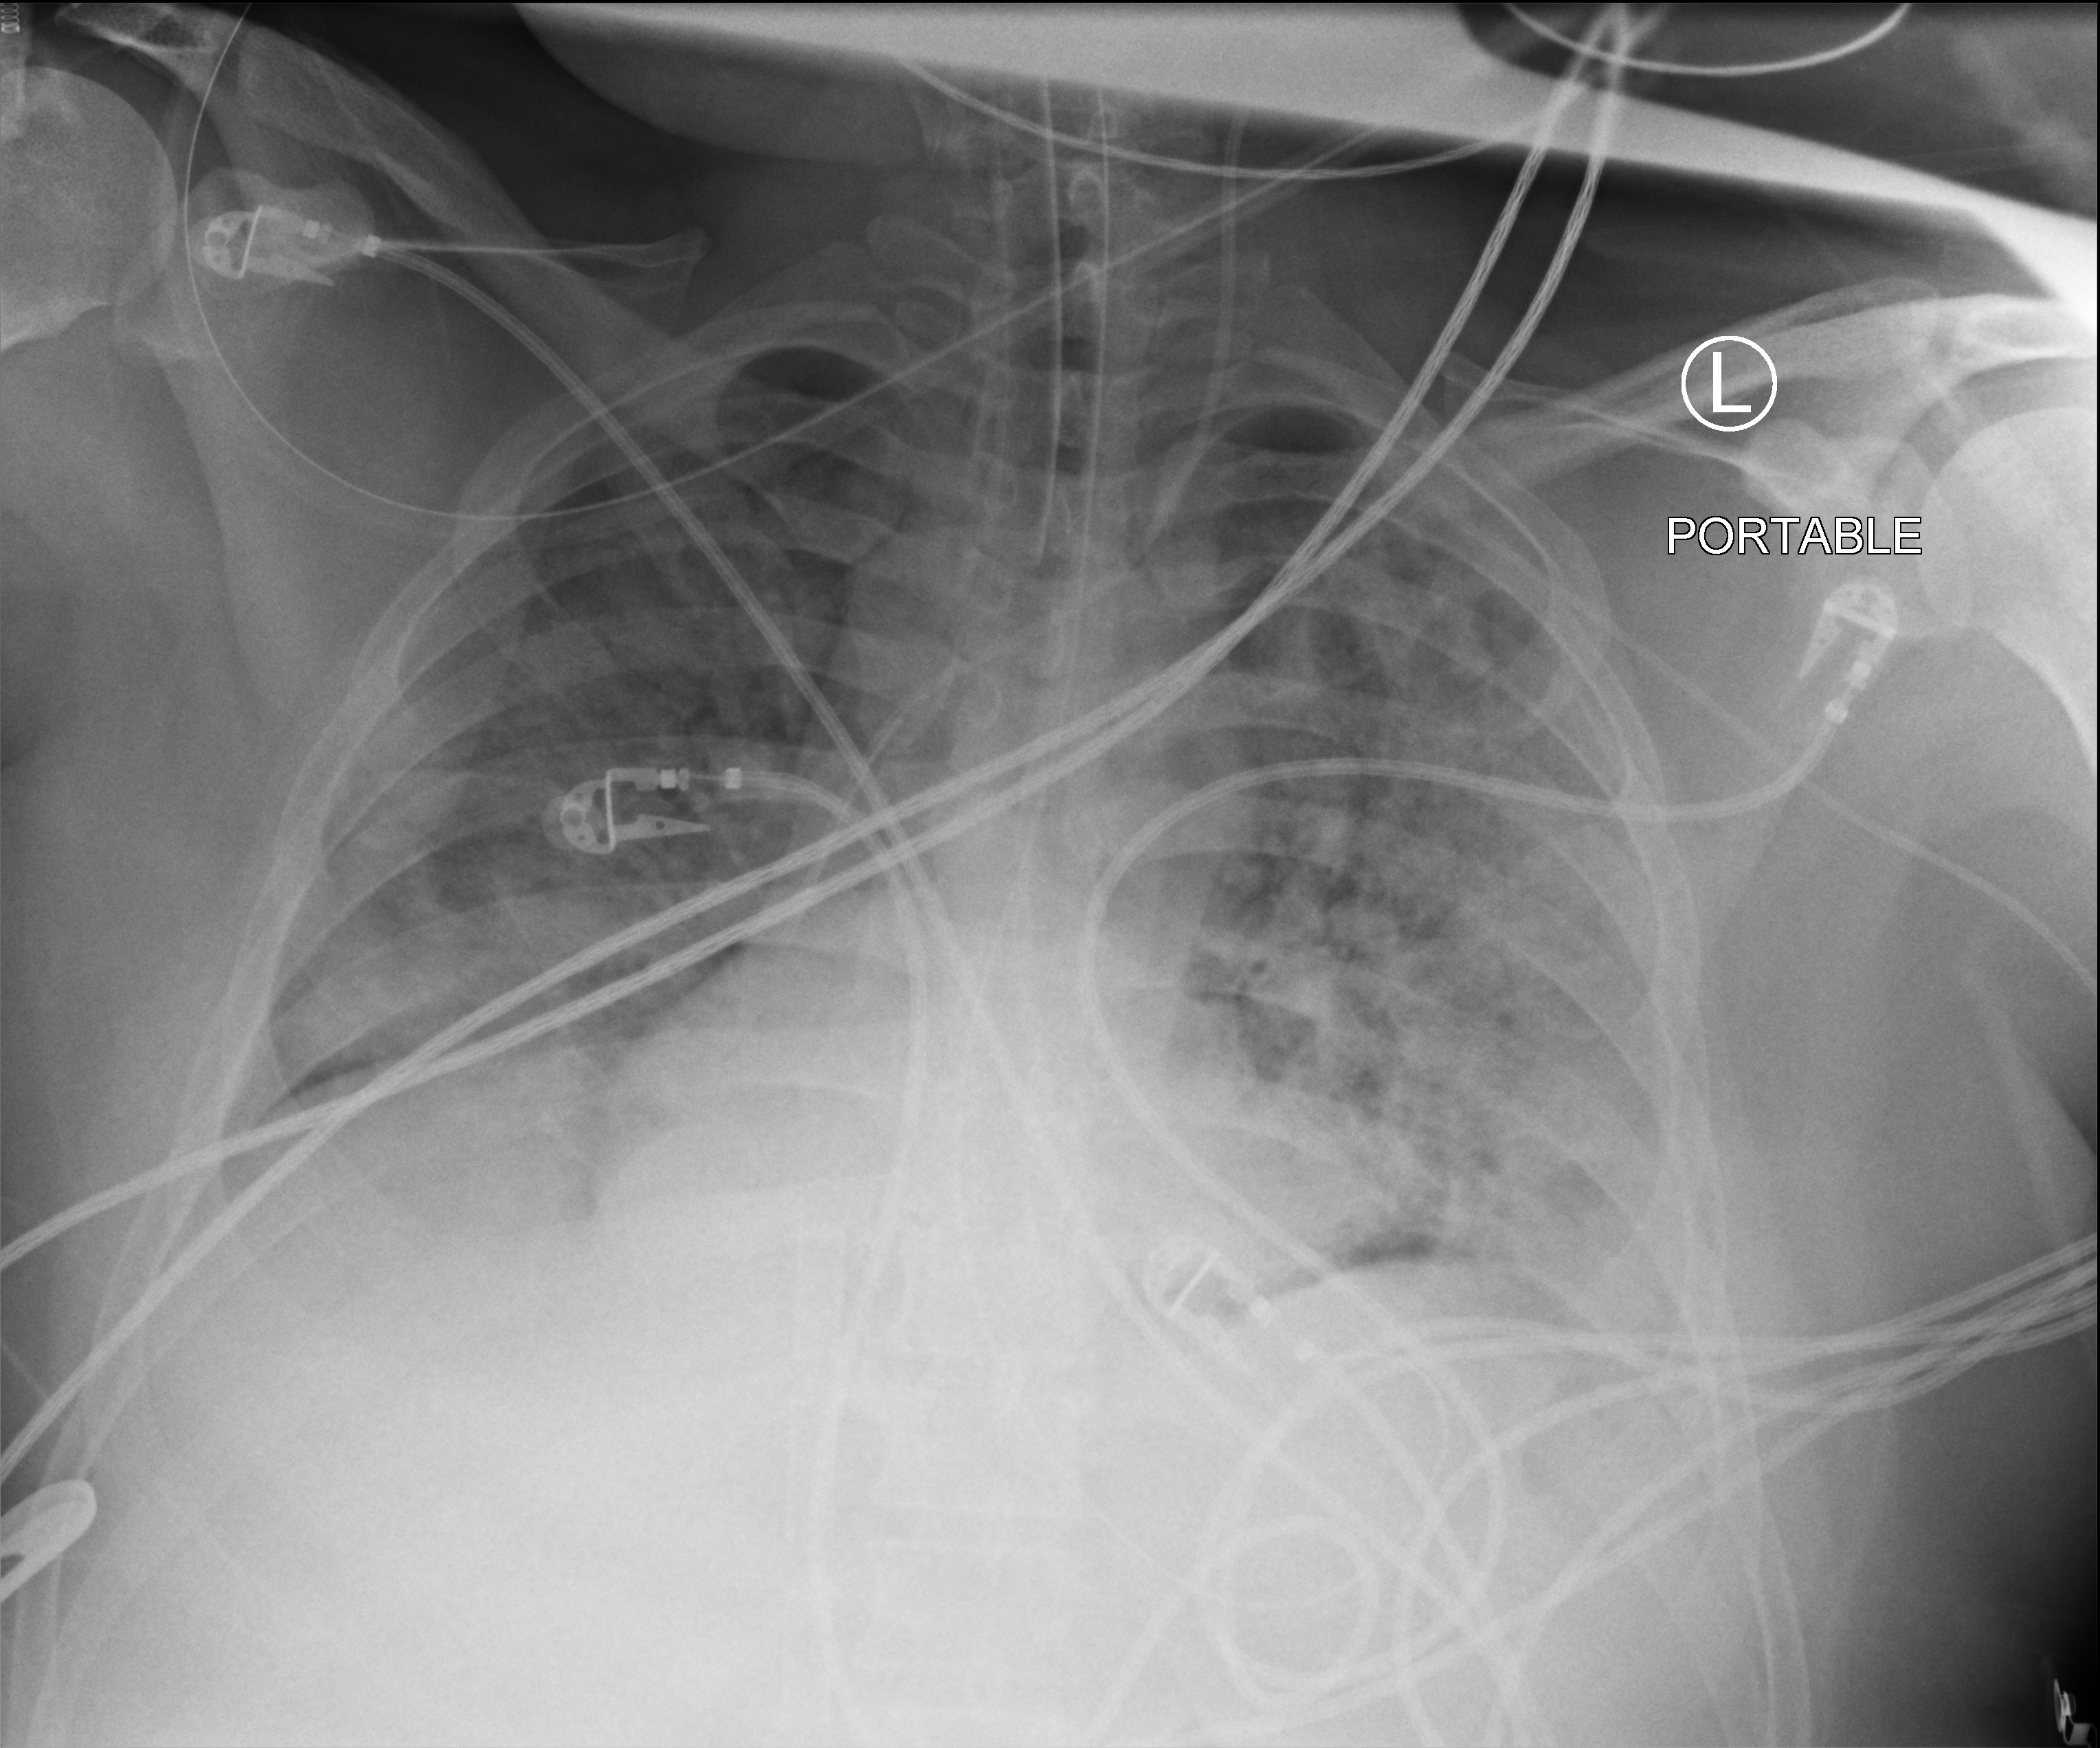
Chest X-ray (portable). Patient hospitalised with COVID-19, aged 18–59 years.
Admission-level facts for this patient (not findings on this image; timing relative to this image not recorded): COPD (admission record): no; smoking status (admission record): never.